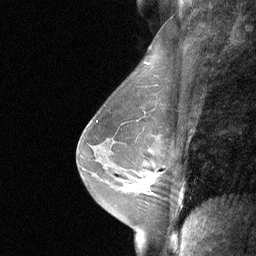
Breast MRI (dynamic contrast-enhanced), one sagittal slice. Position 42 of 64 along the scan axis. Dynamic contrast-enhanced study with each time point stored as its own series, time point 2 of 3 at this slice position (early post-contrast, ordered by acquisition time). 1.5 T. TE 4.8 ms, TR 27 ms. 2 mm slice thickness. 256 × 256 image matrix, field of view 200 × 200 mm. Patient: female, 48 years. Case-level facts recorded for this patient, not image findings: setting: breast cancer imaged before/during neoadjuvant chemotherapy; receptor status: HR-positive, HER2-negative.
Annotated regions visible in this slice (semi-automatically segmented with operator editing):
- analysis volume of interest (the breast-tissue region the enhancement analysis was run in; not a lesion): bounding box [x1, y1, x2, y2] px = [131, 165, 168, 200]
- tumour enhancement mask (voxels above the 90 % enhancement threshold inside the analysis volume of interest): [142, 175, 155, 193]